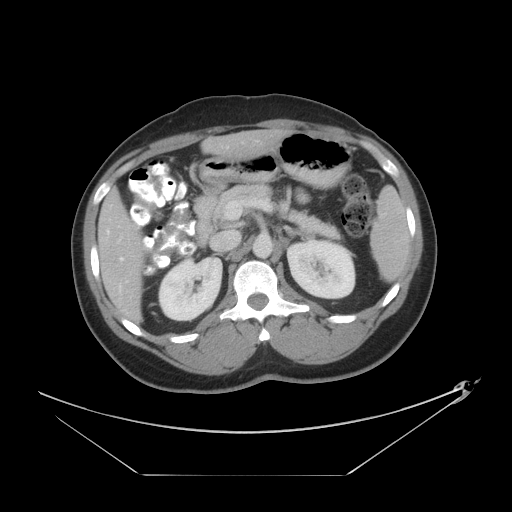
Contrast-enhanced abdominal CT, one axial slice. Slice 22 of 44 in the series (ordered by position). Reconstruction kernel STANDARD. Intravenous contrast given. Soft-tissue window (W 400 / L 40 HU). 5 mm slice thickness. 512 × 512 image matrix, field of view 466 × 466 mm. Male patient, age 49 years. Case-level facts recorded for this patient, not image findings: diagnosis: colorectal cancer liver metastases, imaged before liver resection; multiple liver metastases: no; largest metastasis: 8.5 cm; disease in both lobes: yes.
Structures marked on this image (outlined manually by an expert reader):
- hepatic veins: bounding box <120,147,228,261> (left, top, right, bottom; pixels)
- liver: <97,130,288,324>
- planned liver remnant (the part of the liver to remain after resection): <221,130,289,158>
- portal vein (with intrahepatic branches): <107,230,110,234>